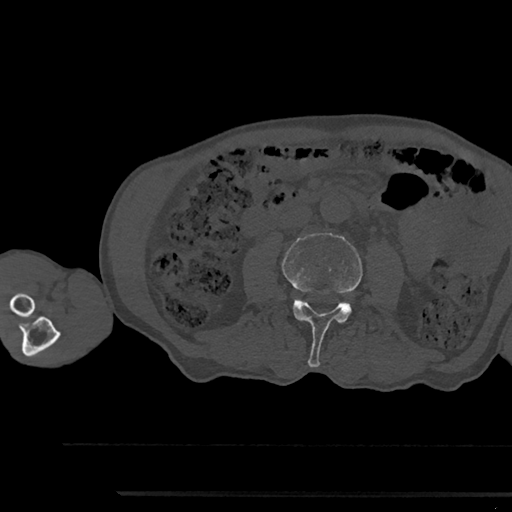
CT including the spine, one axial slice. Slice 480 of 797 in the series (ordered by position). Reconstruction kernel Br40s/3. Bone window (W 1800 / L 400 HU). 0.5 mm slice thickness. 512 × 512 image matrix, field of view 367 × 367 mm. Patient: male, 79 years. From the clinical record (not read from this slice): primary cancer: prostate.
Annotated regions visible in this slice (semi-automatically segmented with operator editing):
- L3 vertebra: bounding box <281,233,362,367> (left, top, right, bottom; pixels)